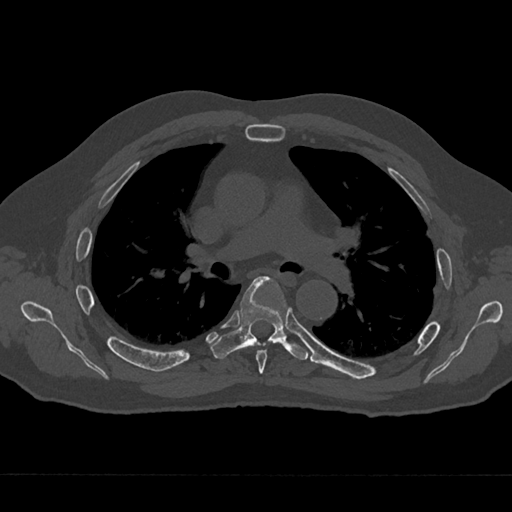
CT including the spine, one axial slice; slice 443 of 797 in the series (ordered by position); reconstruction kernel Br40s/3; bone window (W 1800 / L 400 HU); 0.5 mm slice thickness; 512 × 512 image matrix. Patient: male, 75 years. From the clinical record (not read from this slice): primary cancer: renal; vertebrae with lytic lesions (as recorded): T4.
Structures marked on this image (semi-automatic segmentation, software-assisted and operator-edited):
- T5 vertebra: bounding box [x1, y1, x2, y2] px = [256, 296, 286, 374]
- T6 vertebra: [212, 276, 309, 360]